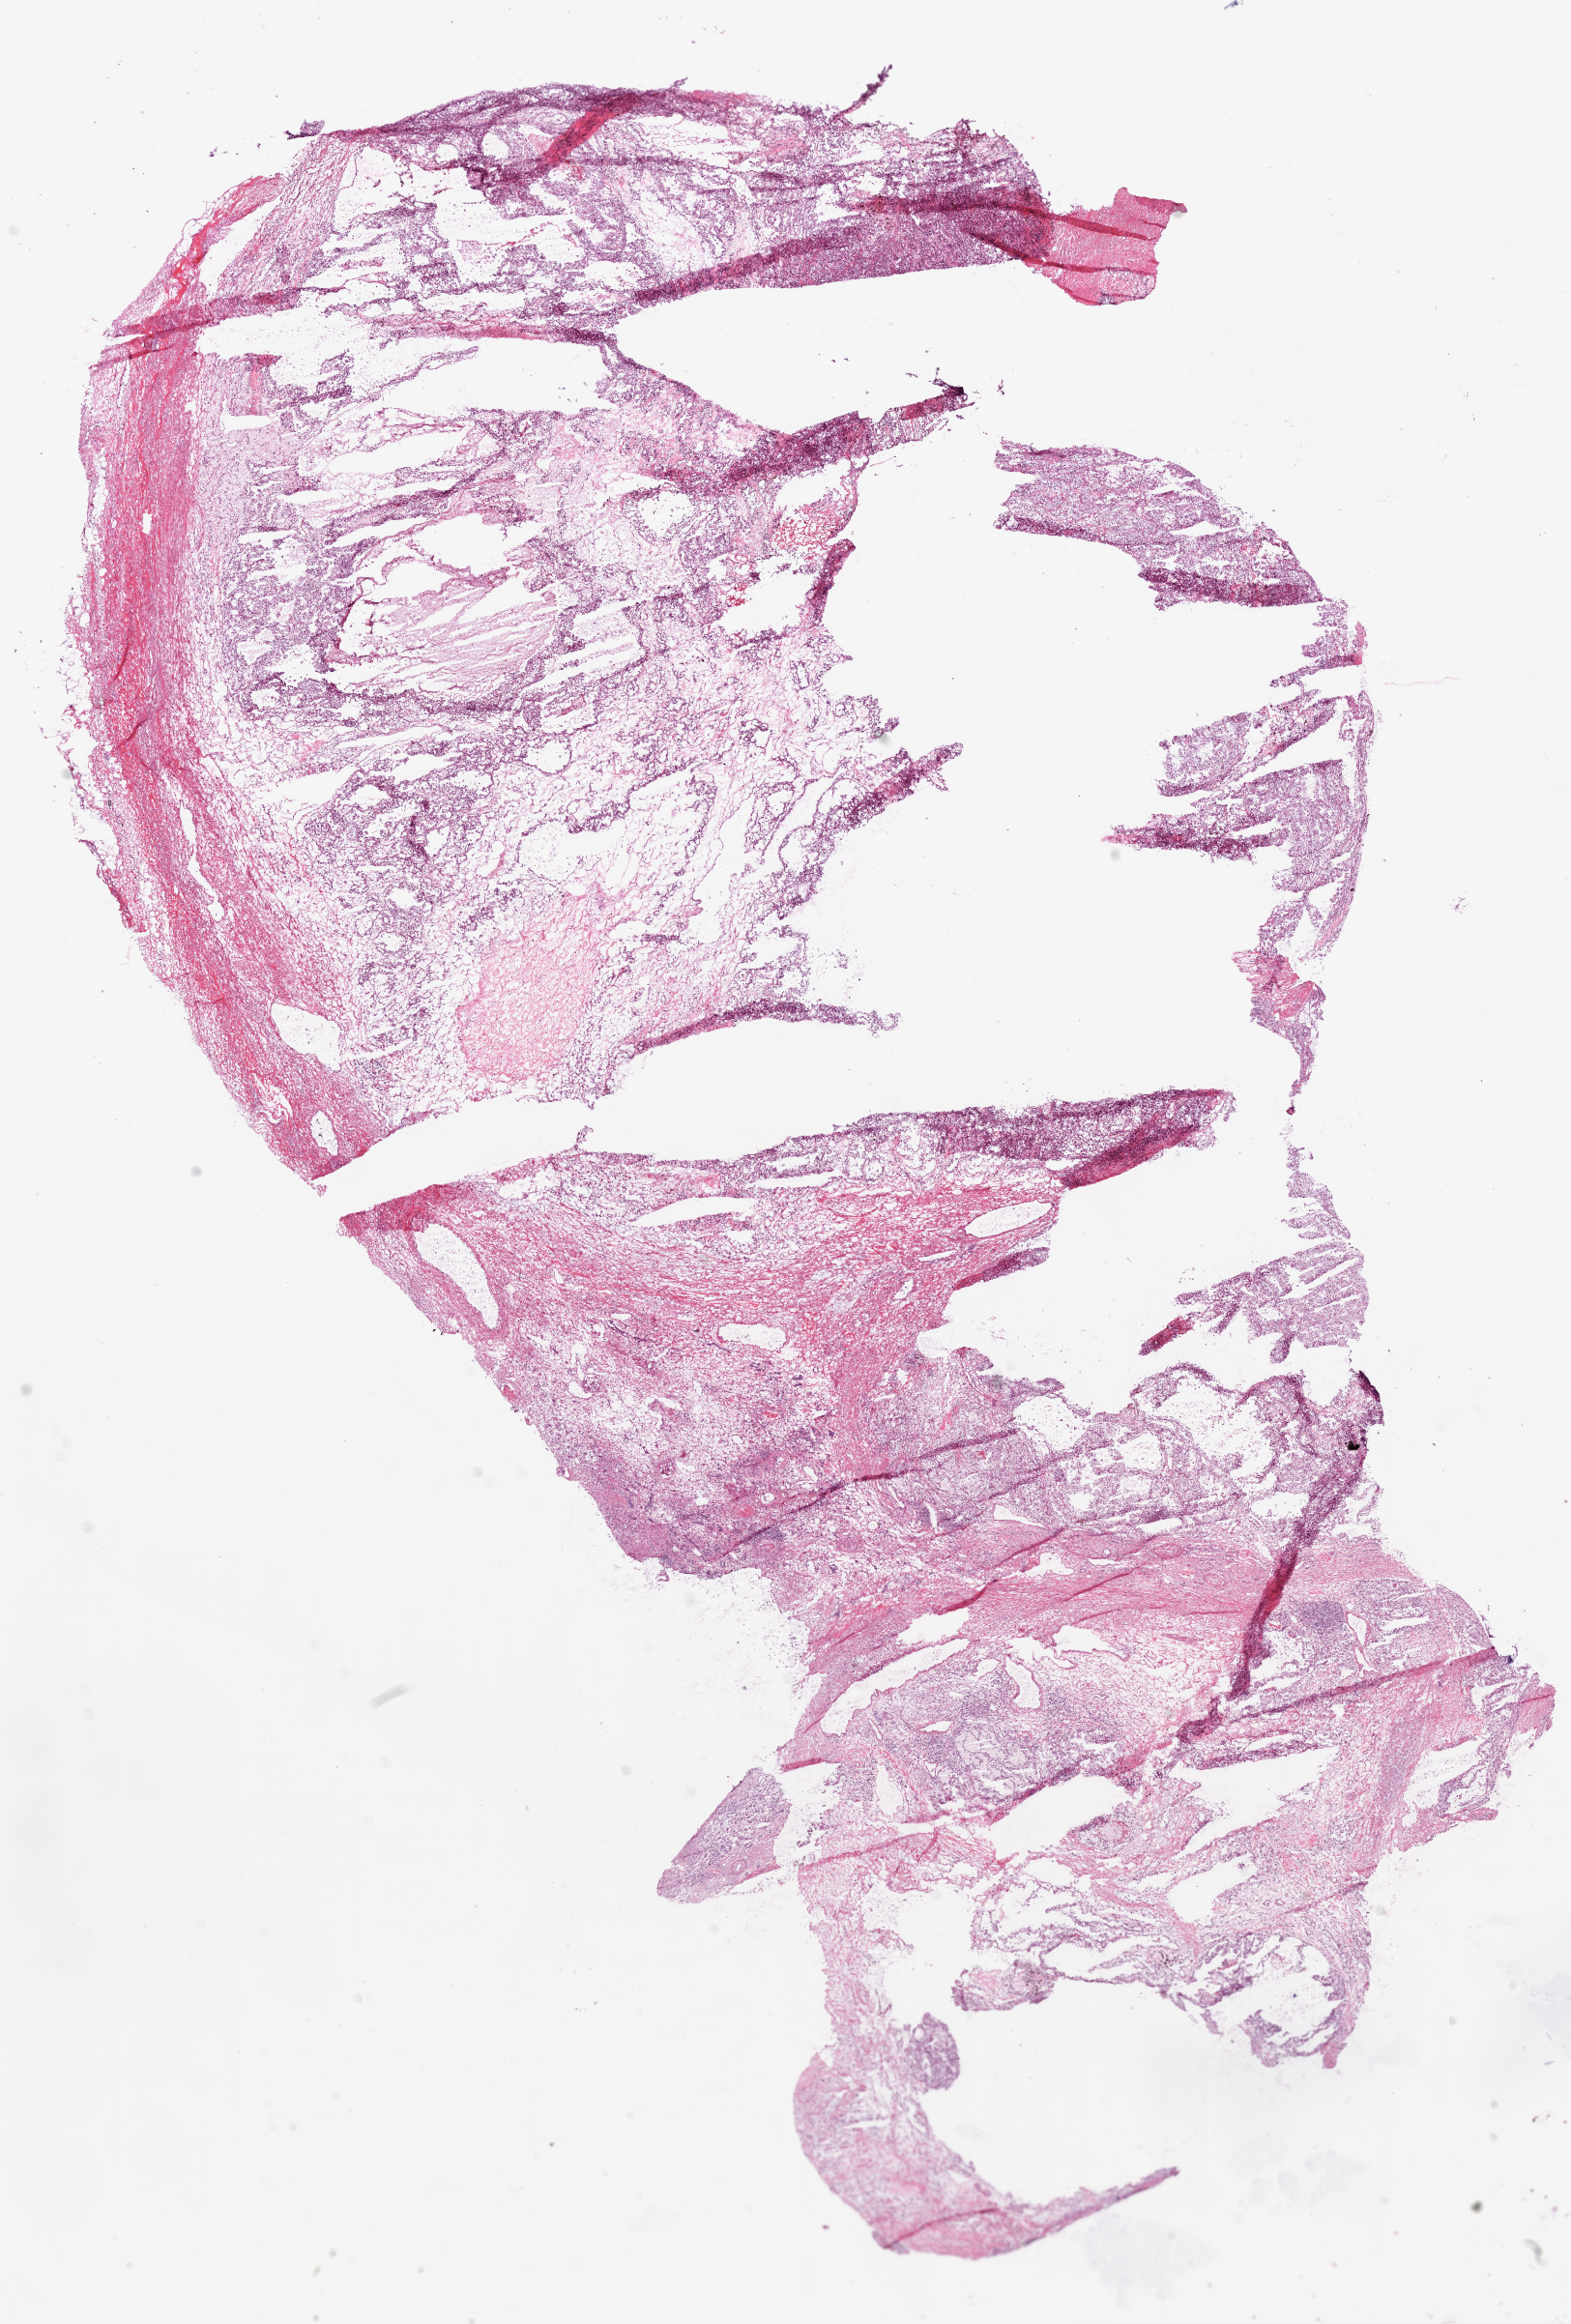
Digitized H&E tissue section (whole slide), a low-resolution overview of the entire scanned area, about 13.0 x 19.3 mm (slide scanned at 20x). Frozen section. Primary tumour sample from the kidney. Male patient; age at initial diagnosis 67 years. Histologic grade: G2 (moderately differentiated). Pathologist review of this section (percent, as recorded): tumour cells 60%, tumour nuclei 80%, normal cells 0%, stromal cells 40%, necrosis 0%.
Diagnosis: Clear cell adenocarcinoma, NOS. Lymph nodes positive (case pathology): 0 of 3 examined. TNM: T3a N0 M0. AJCC pathologic stage: III.